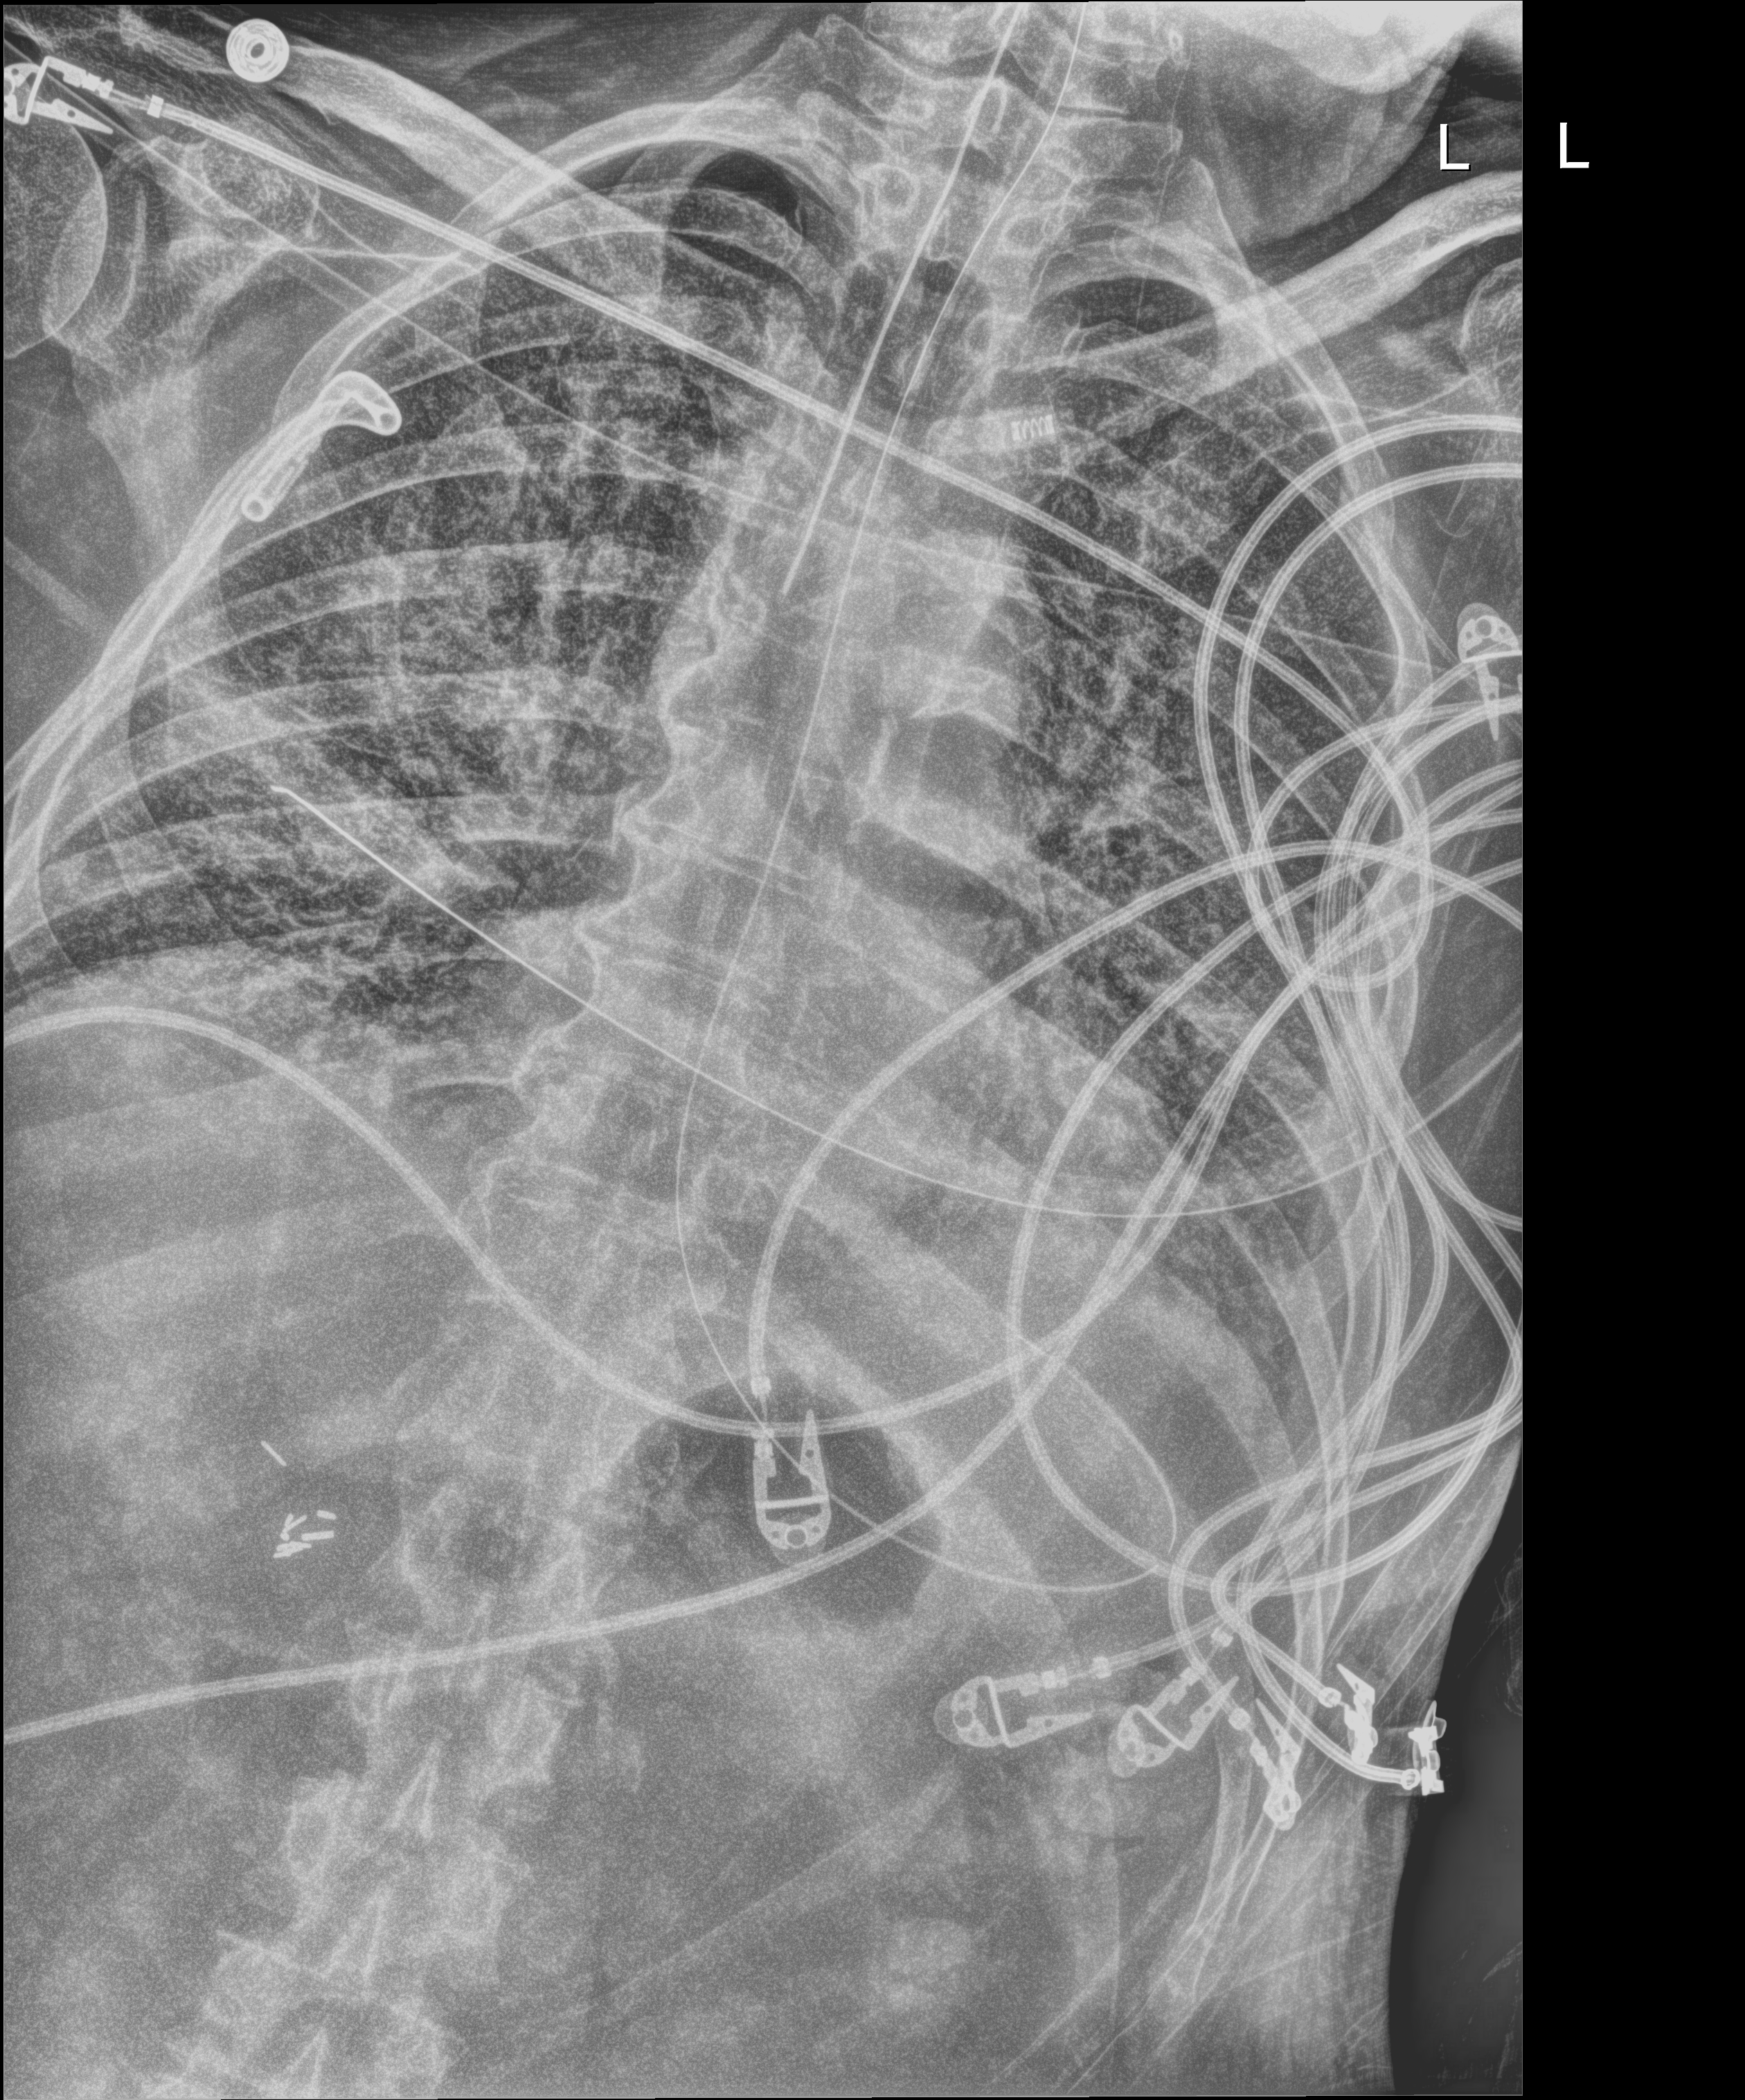
Chest X-ray (portable); anteroposterior (AP) projection. Male patient hospitalised with COVID-19, age 75–90 years.
Hospital-stay facts (about this admission, not read from this image; timing relative to this image not recorded):
- admitted to intensive care during this hospital stay: yes
- other chronic lung disease (admission record): no
- mechanically ventilated during this hospital stay: yes